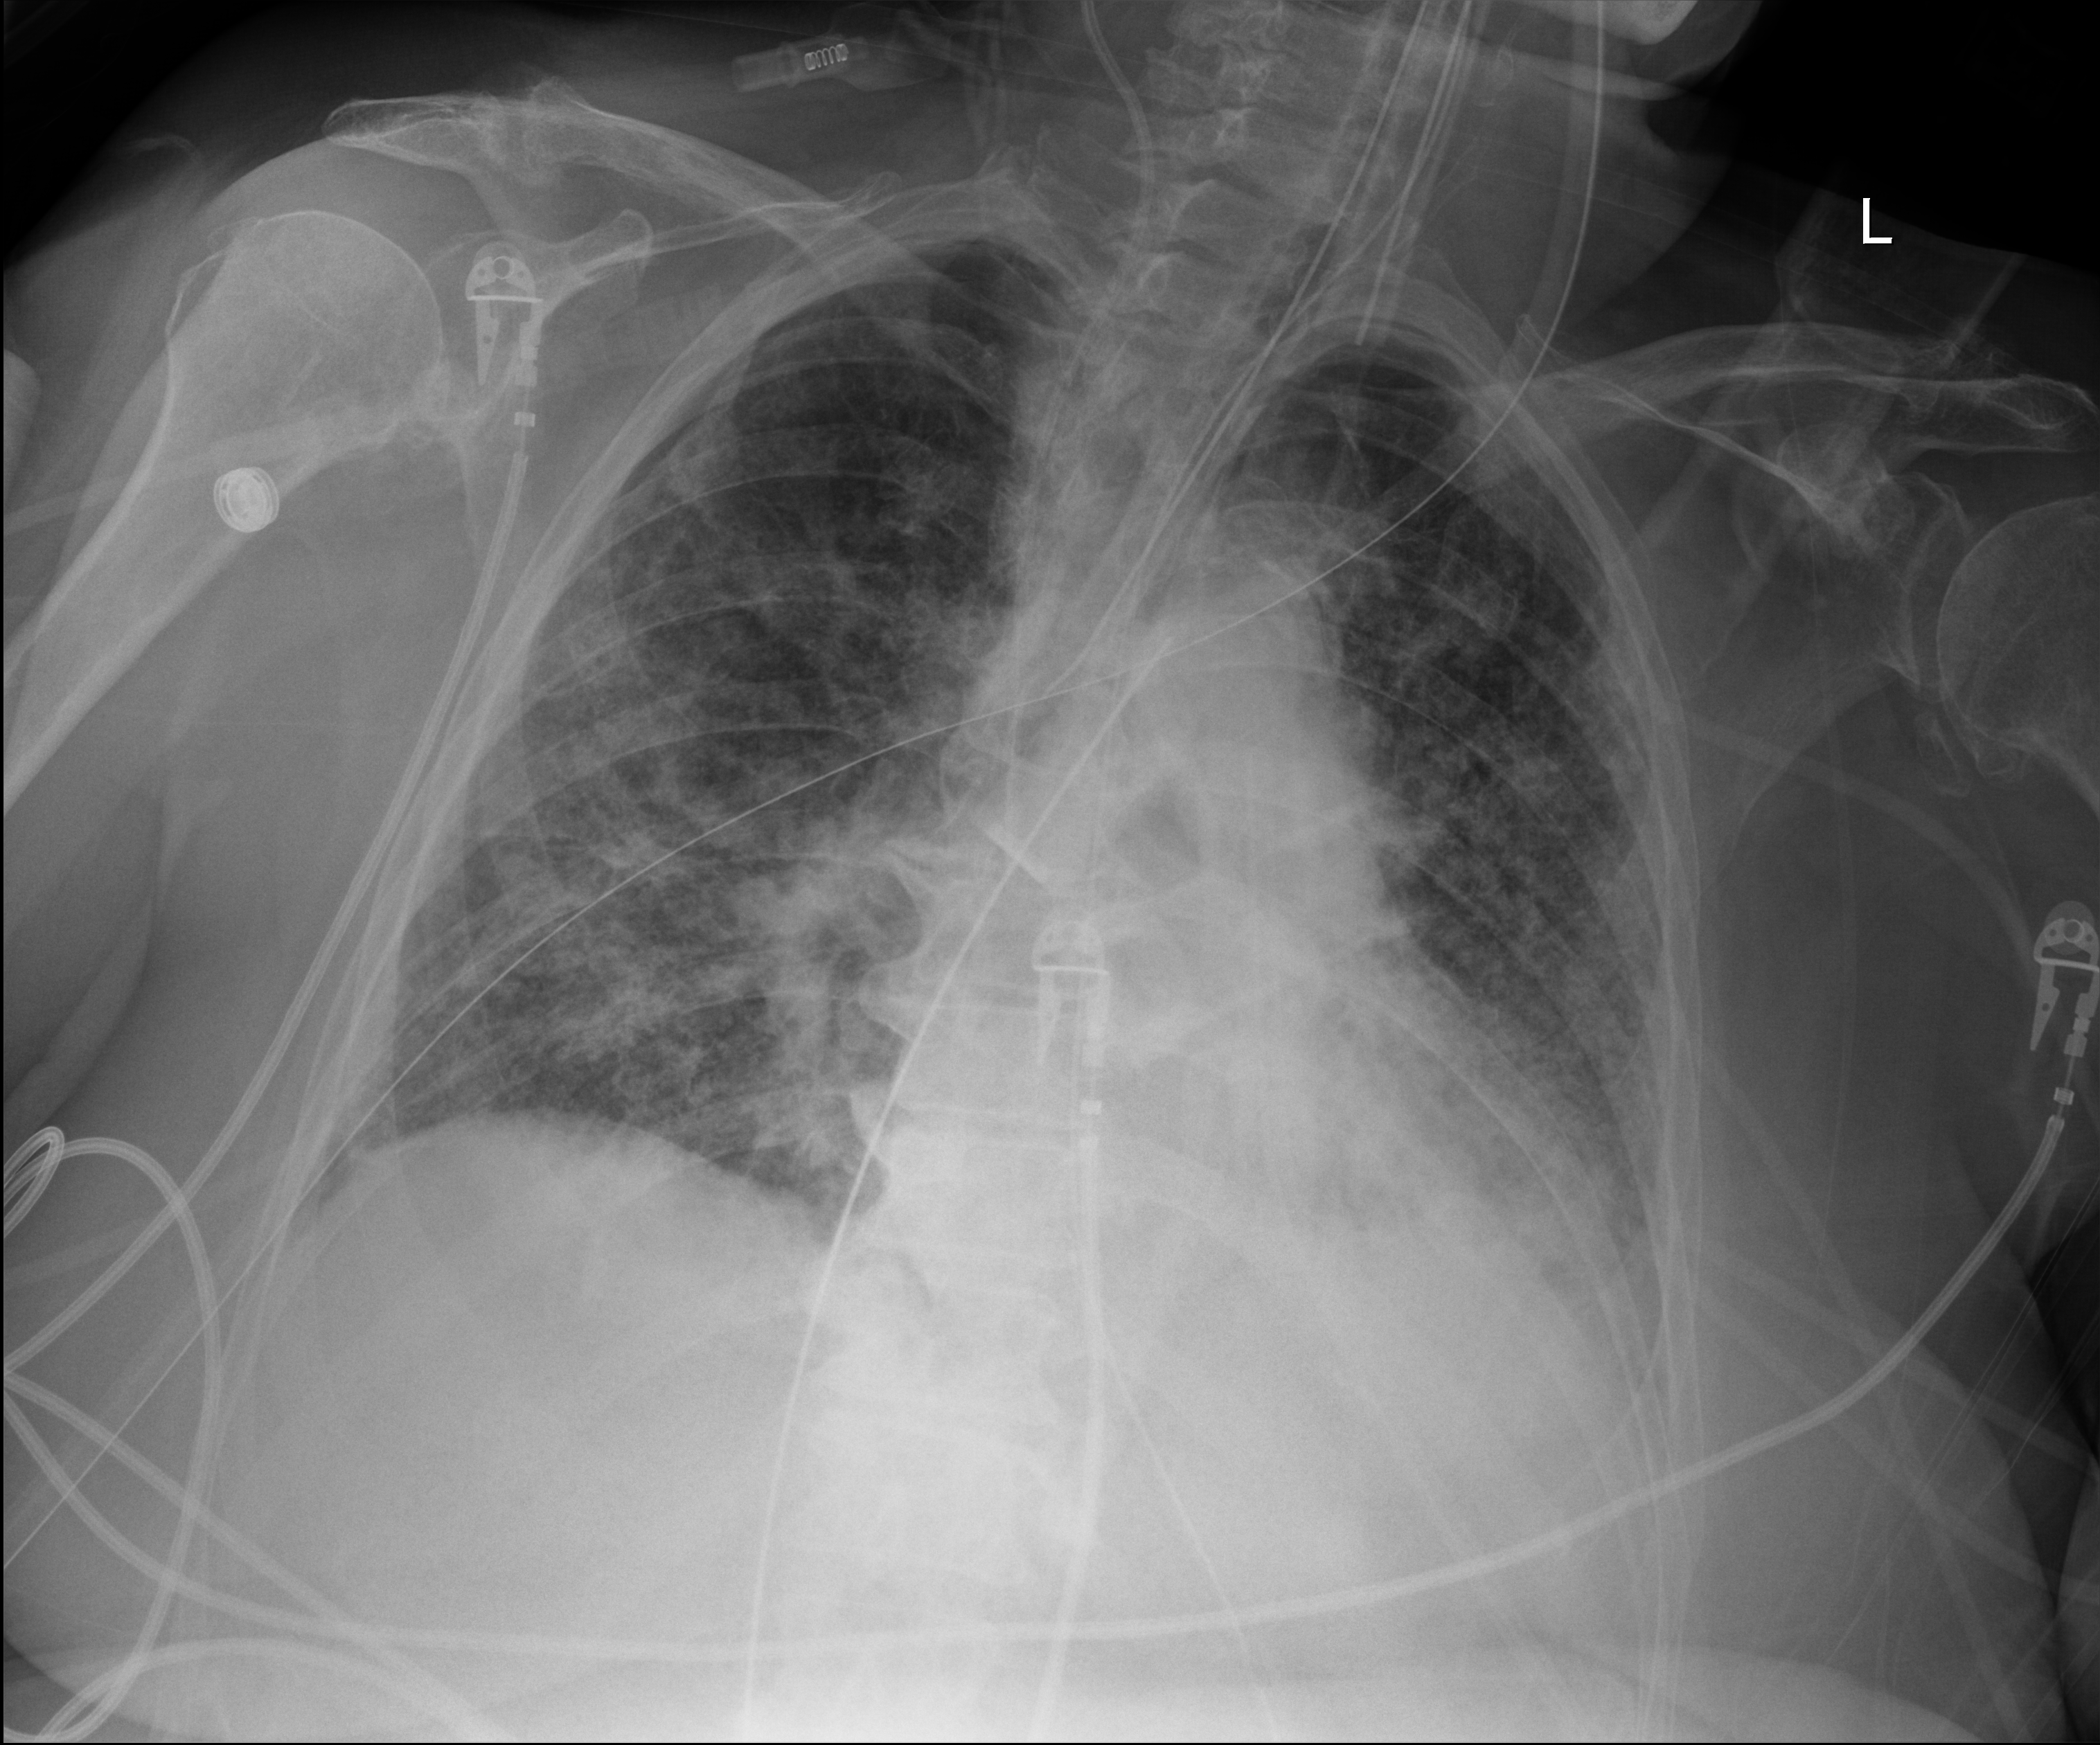
Chest X-ray (portable), anteroposterior (AP) projection. Female patient hospitalised with COVID-19, age 75–90 years.
From the hospital-stay record, not from the radiograph (when in the stay this image was taken is not recorded): smoking status (admission record): former; chronic kidney disease (admission record): no.